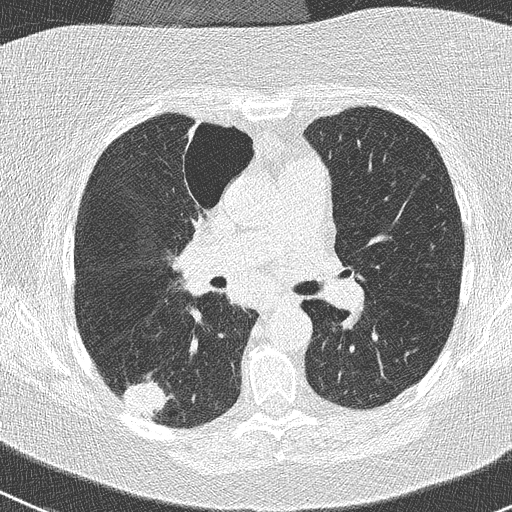
Low-dose screening chest CT, one axial slice; position 151 of 261 along the scan axis; reconstruction kernel B50f; 120 kVp; lung window (W 1500 / L -600 HU); 2 mm slice thickness; 512 × 512 image matrix, field of view 310 × 310 mm.
Annotated regions visible in this slice (manually delineated by an expert):
- lesion 1 (tumor, lower lobe of right lung): bounding box <123,381,167,420> (left, top, right, bottom; pixels)